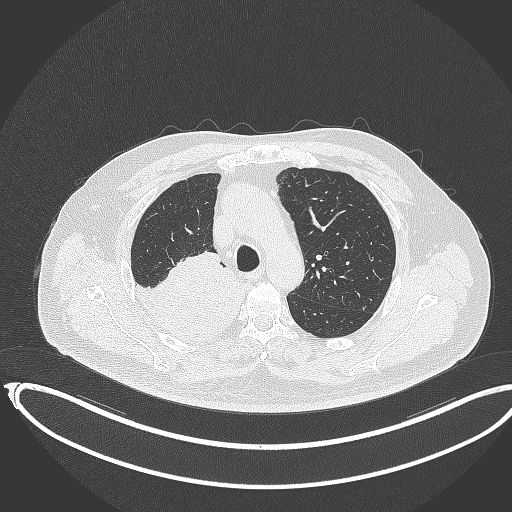
Chest CT, one axial slice. Position 263 of 403 along the scan axis. Reconstruction kernel B70f. 120 kVp. Lung window (W 1500 / L -600 HU). 512 × 512 image matrix, field of view 436 × 436 mm. Patient: male, 68 years. Case-level facts recorded for this patient, not image findings: clinical TNM (as recorded): T2a N0 M0.
Structures marked on this image (rectangle marked by the reading radiologist):
- lung tumour (recorded histology: adenocarcinoma): box from (x=131, y=246) to (x=244, y=344) px